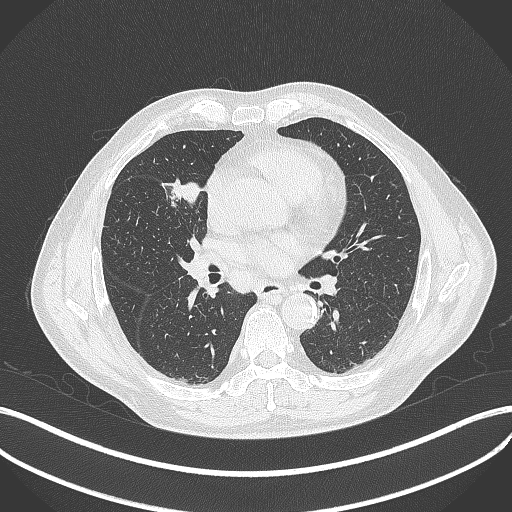
Chest CT, one axial slice; position 203 of 429 along the scan axis; reconstruction kernel B70f; 120 kVp; lung window (W 1500 / L -600 HU); 1 mm slice thickness; 512 × 512 image matrix, field of view 400 × 400 mm. Patient: male, 61 years. From the clinical record (not read from this slice): clinical TNM (as recorded): T2b N1 M0.
Annotated regions visible in this slice (rectangle marked by the reading radiologist):
- lung tumour (recorded histology: squamous cell carcinoma): bounding box (x1, y1, x2, y2) in pixels: (165, 178, 205, 208)